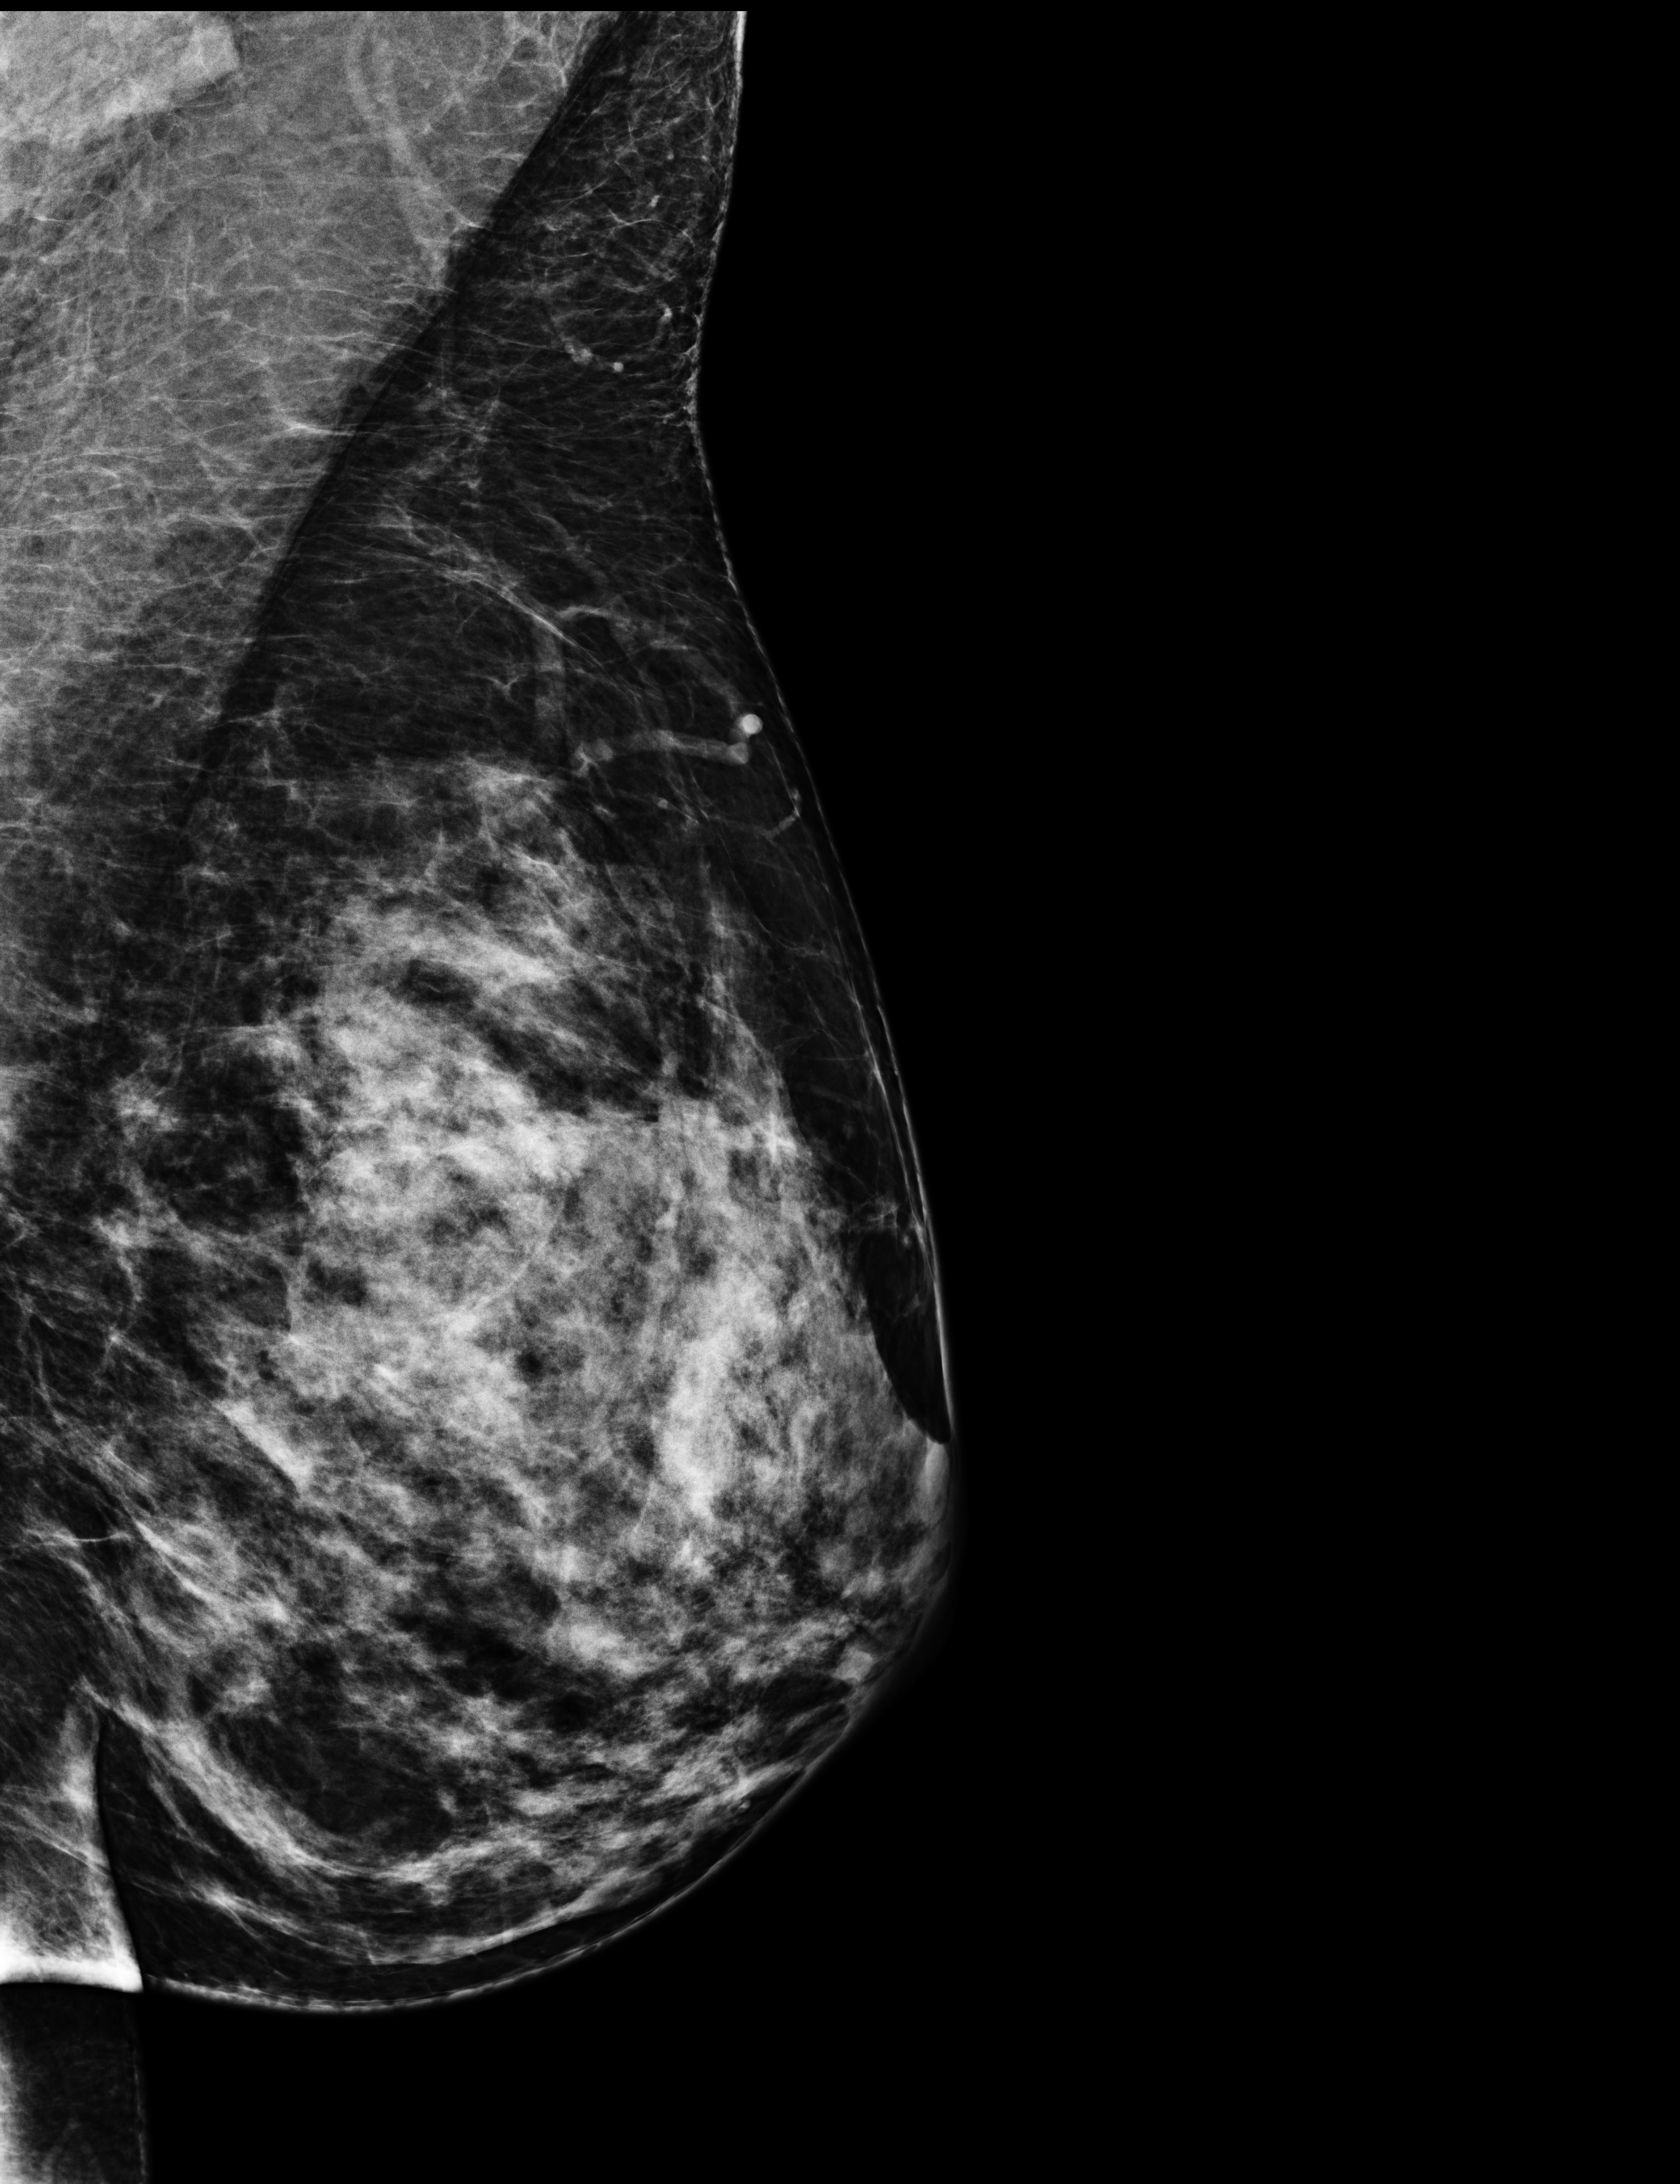
Digital mammogram (FFDM); left breast; mediolateral oblique (MLO) view; annual screening mammography examination. Patient: female, 42 years.
Breast density at the screening exam (both breasts): extremely dense (BI-RADS density category d). Final BI-RADS assessment for this screening round (tomosynthesis exam, both breasts): category 1. Recall: no recall after this screen.